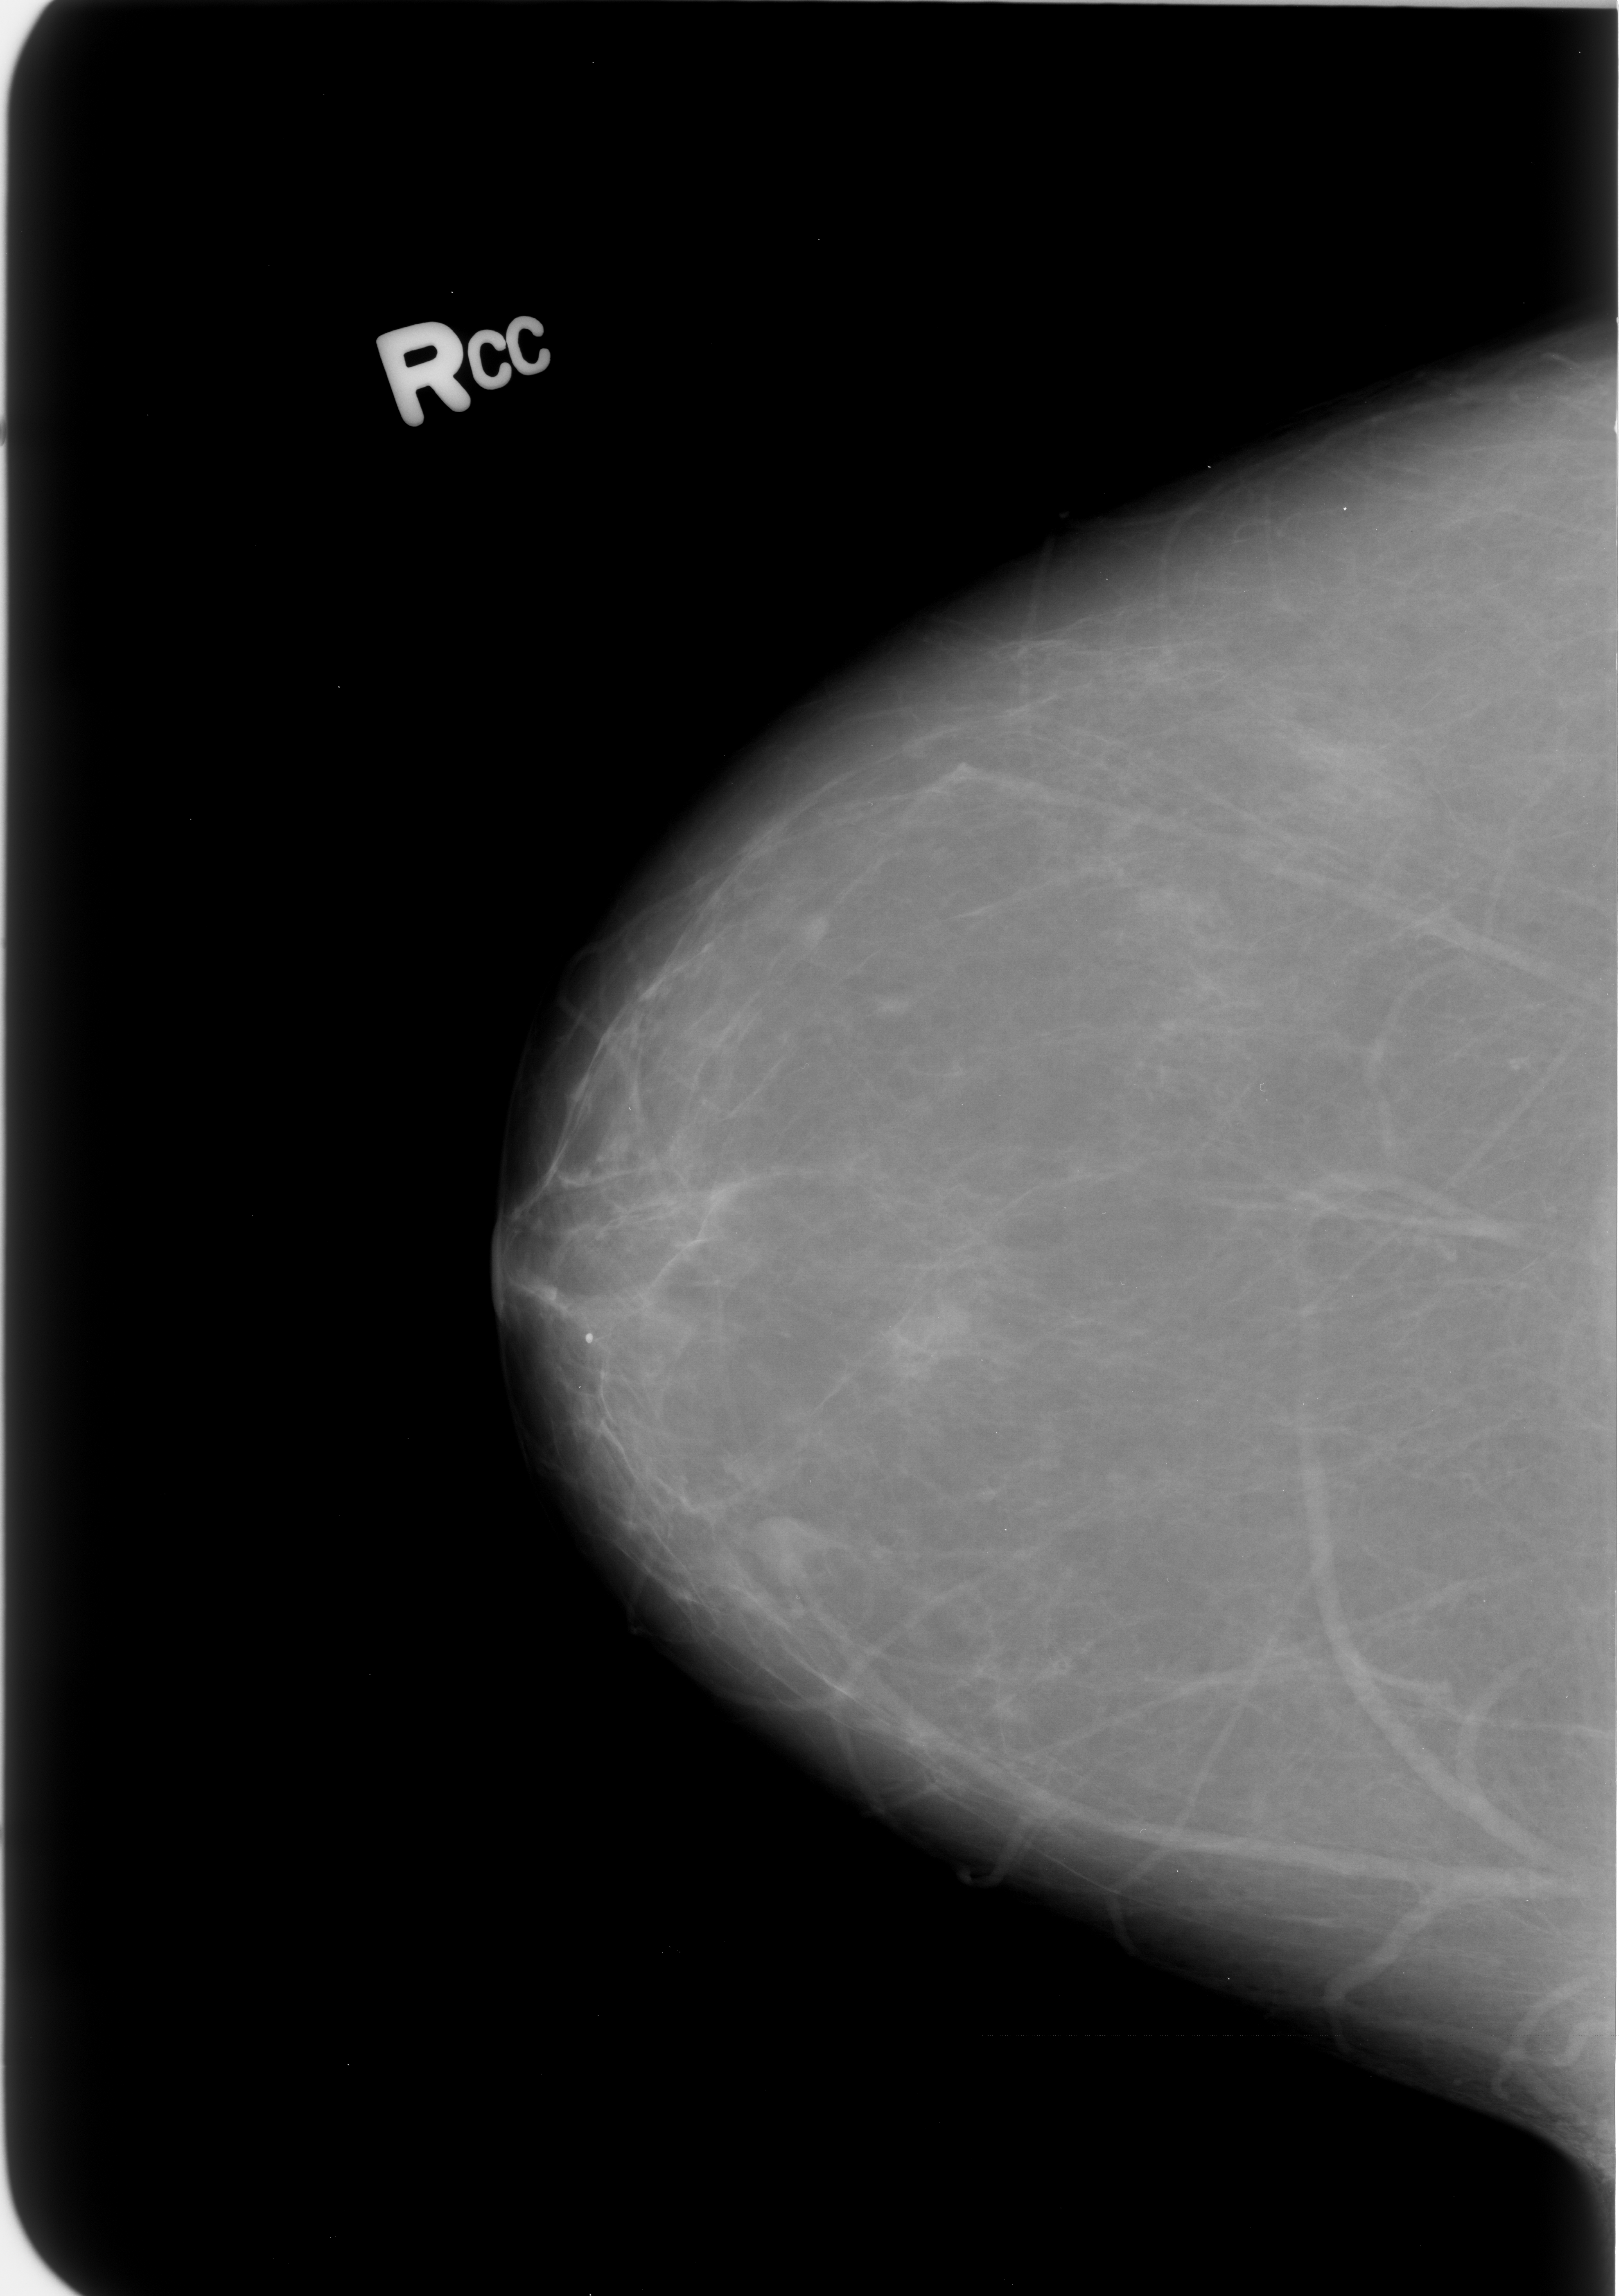
Digitized screen-film mammogram; right breast; CC view; 1621 × 2296 image matrix.
Expert-marked regions of interest on this image (one box per marked abnormality):
- mass, shape lobulated, margins circumscribed / ill defined; BI-RADS assessment category 4; pathology result (as recorded, not read from the image): benign: bounding box [x1, y1, x2, y2] px = [739, 1511, 828, 1589]